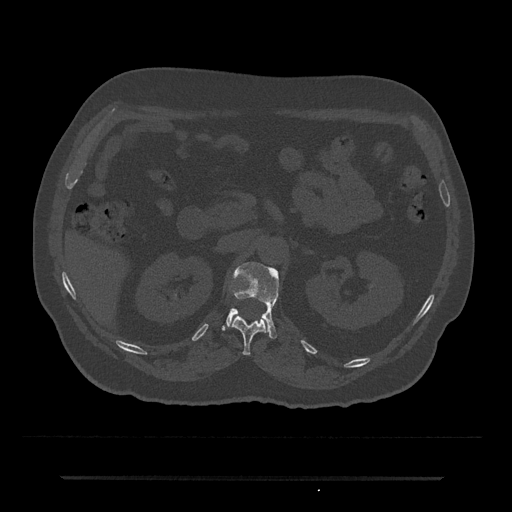
CT including the spine, one axial slice. Position 101 of 797 along the scan axis. 120 kVp. Bone window (W 1800 / L 400 HU). 0.5 mm slice thickness. 512 × 512 image matrix. Patient: male, 69 years. Case-level facts recorded for this patient, not image findings: primary cancer: prostate.
Outlined on this slice (semi-automatically segmented with operator editing):
- L1 vertebra: bounding box <226,262,279,339> (left, top, right, bottom; pixels)
- T12 vertebra: <231,313,268,355>